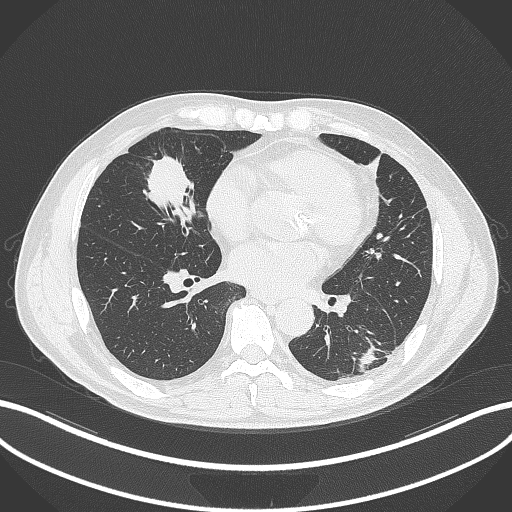
Chest CT, one axial slice. Position 125 of 399 along the scan axis. 120 kVp. Lung window (W 1500 / L -600 HU). 512 × 512 image matrix, field of view 400 × 400 mm. Patient: male, 59 years. From the clinical record (not read from this slice): clinical TNM (as recorded): T2a N1 M0.
Annotated regions visible in this slice (bounding box drawn by a radiologist):
- lung tumour (recorded histology: adenocarcinoma): box from (x=140, y=155) to (x=202, y=220) px